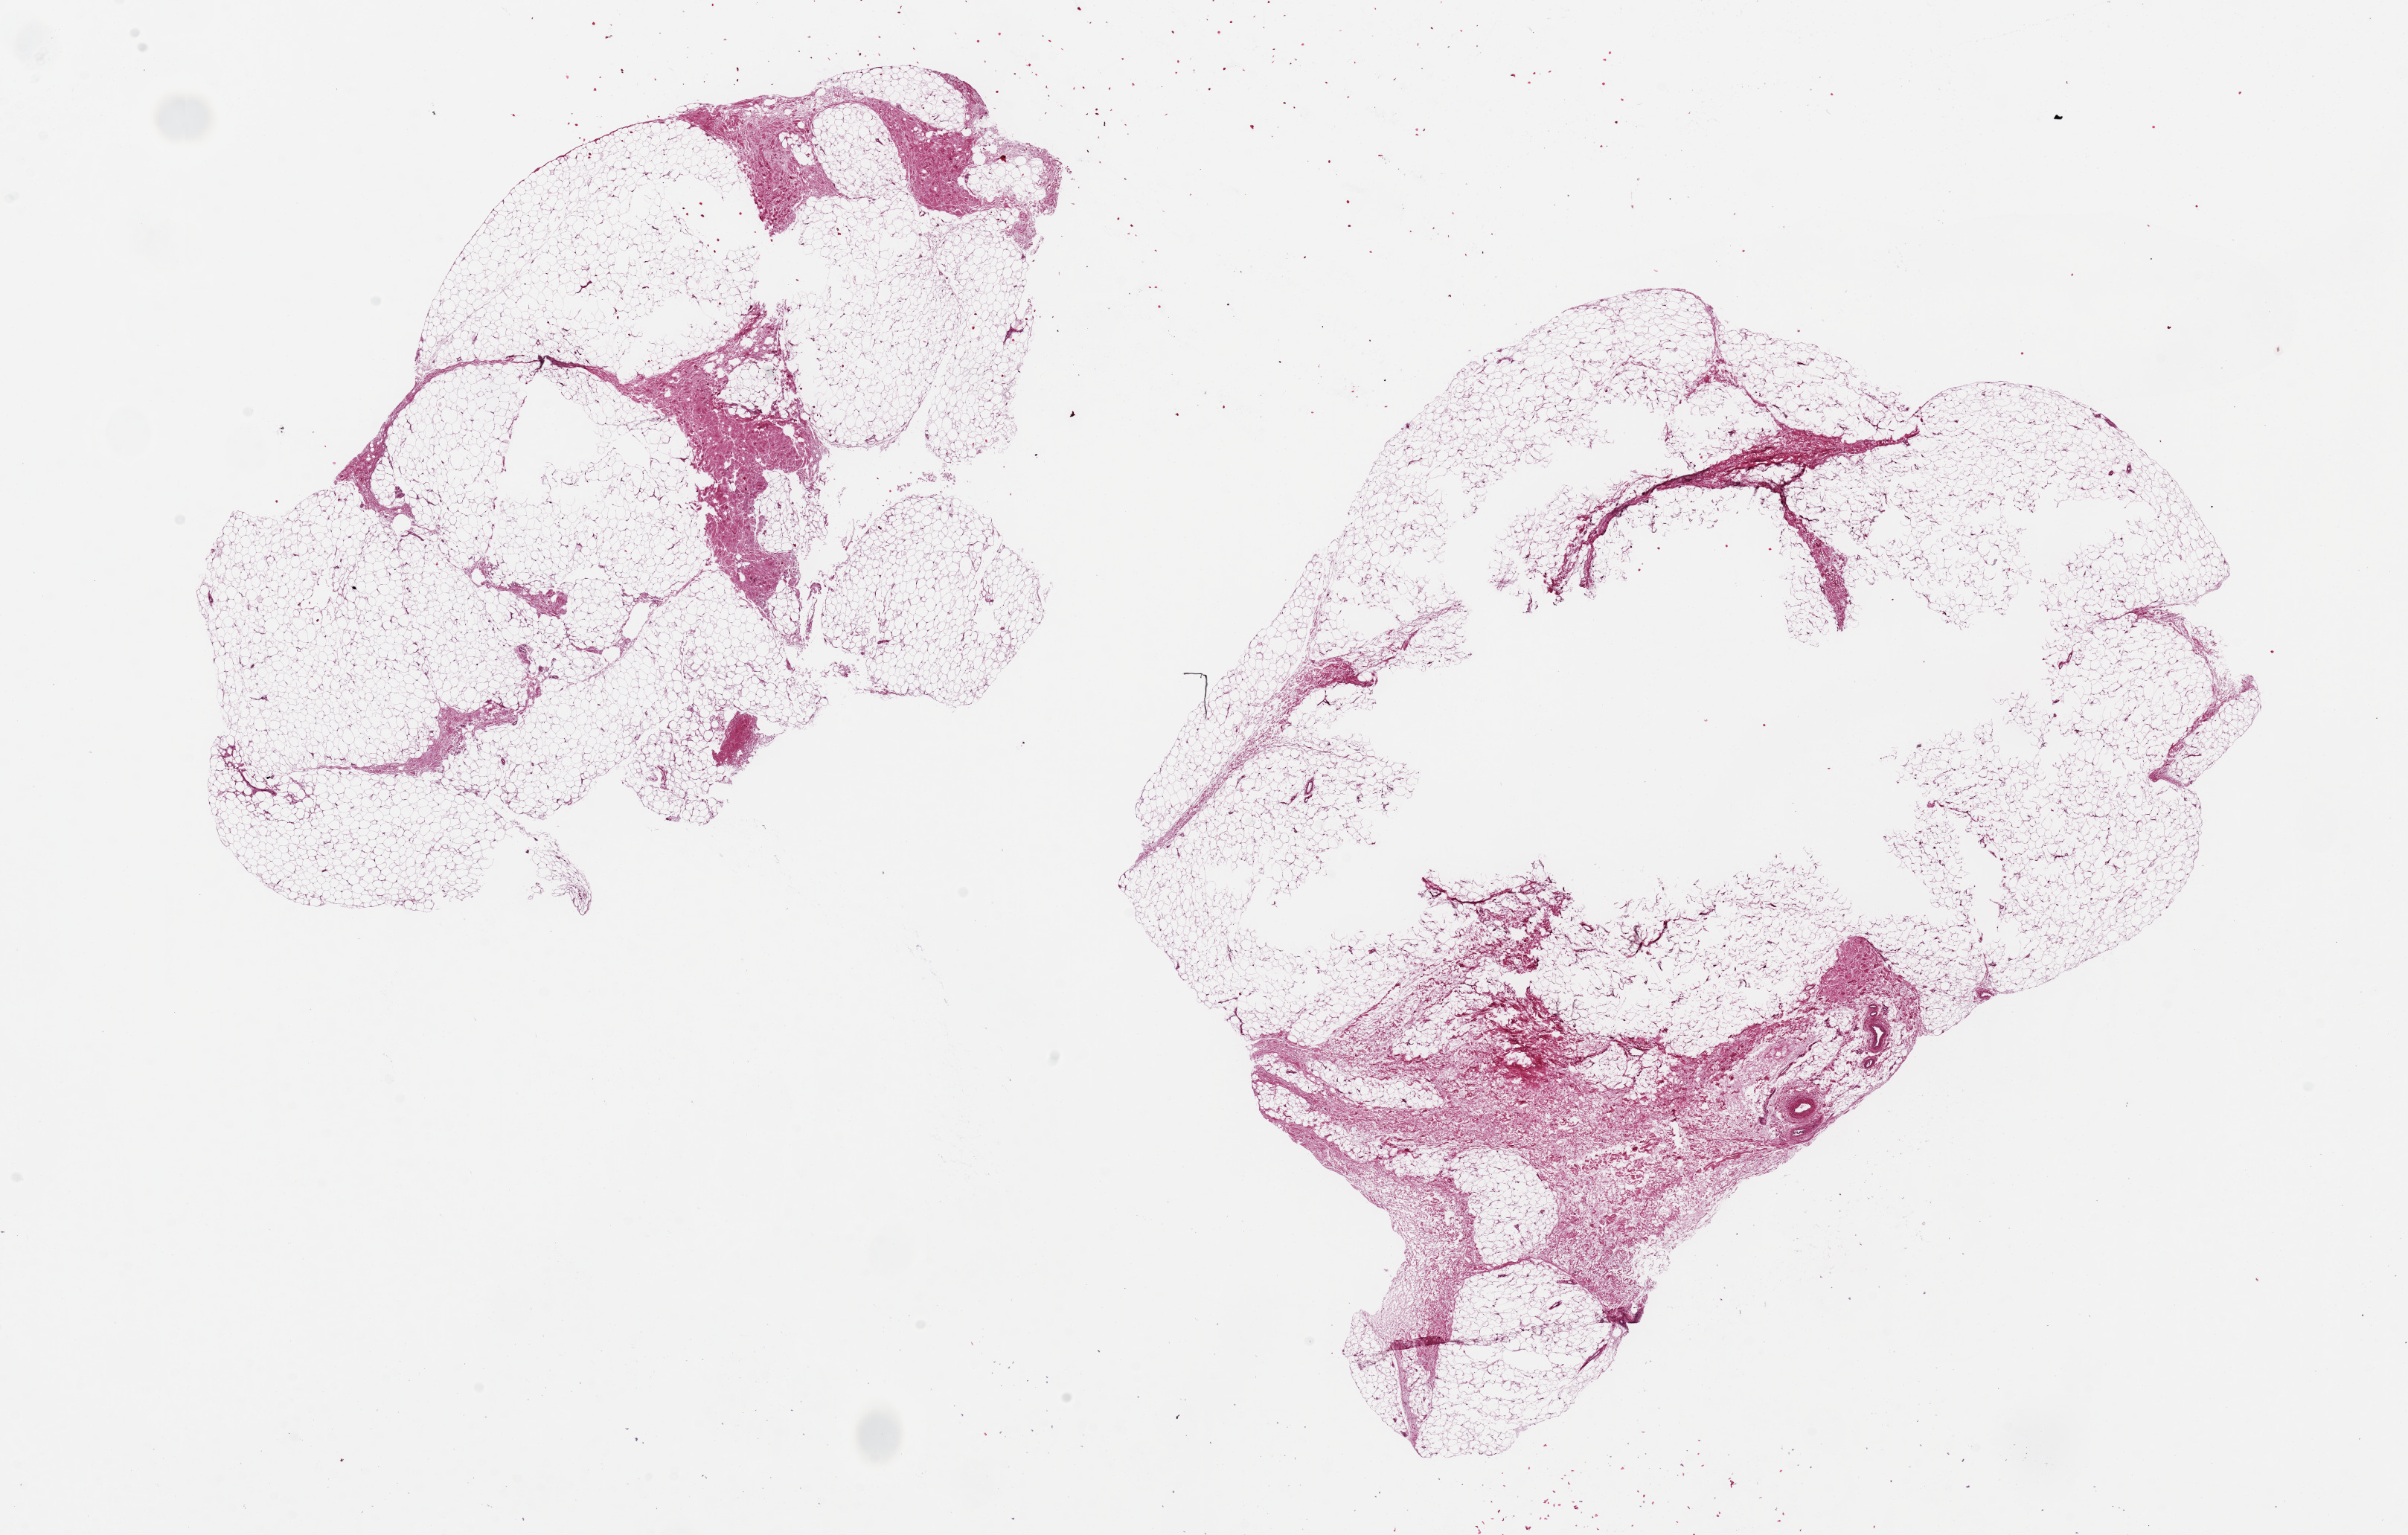
Whole-slide image, H&E stain, a low-resolution overview of the entire scanned area, about 25.6 x 16.3 mm (from a 20x scan), PAXgene-fixed paraffin-embedded (PFPE) section, target tissue: adipose tissue, tissue donor sample. Female donor.
* review note (as recorded): 2 pieces, ~ 10x7mm